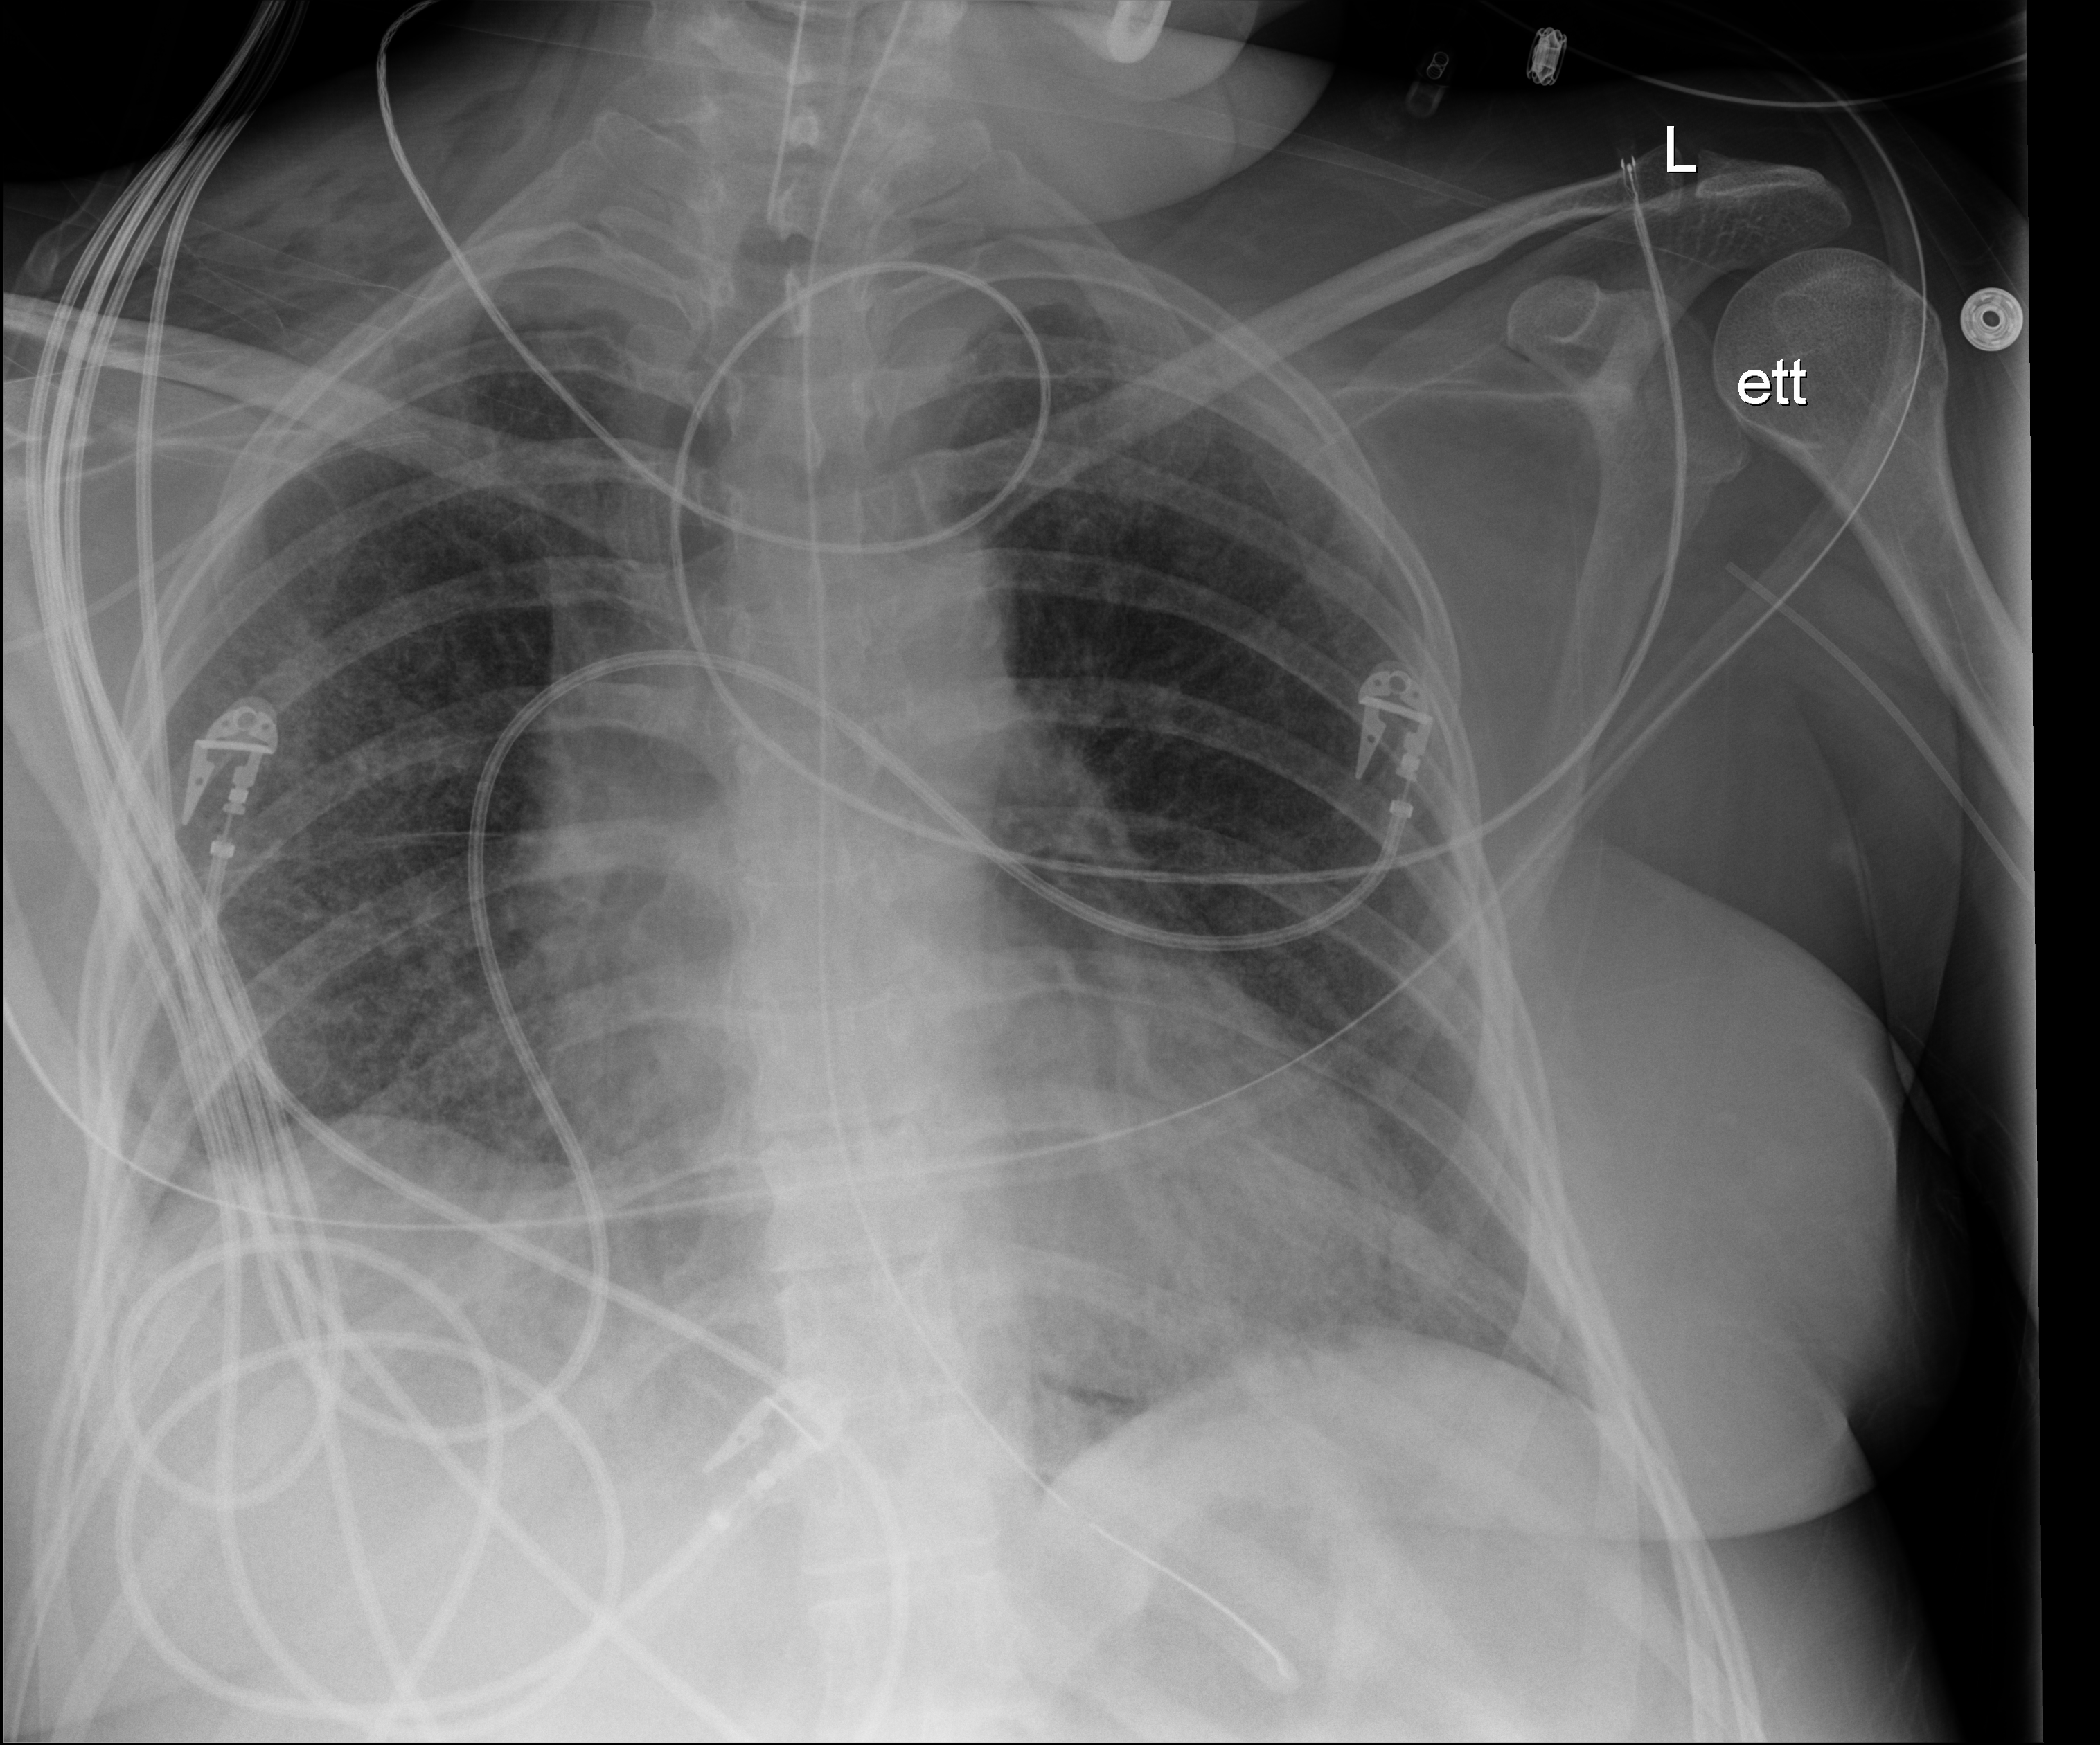
Bedside chest radiograph (digital radiography); anteroposterior (AP) projection. Patient hospitalised with COVID-19; female, aged 18–59 years.
From the hospital-stay record, not from the radiograph (when in the stay this image was taken is not recorded): other chronic lung disease (admission record): yes; smoking status (admission record): former.